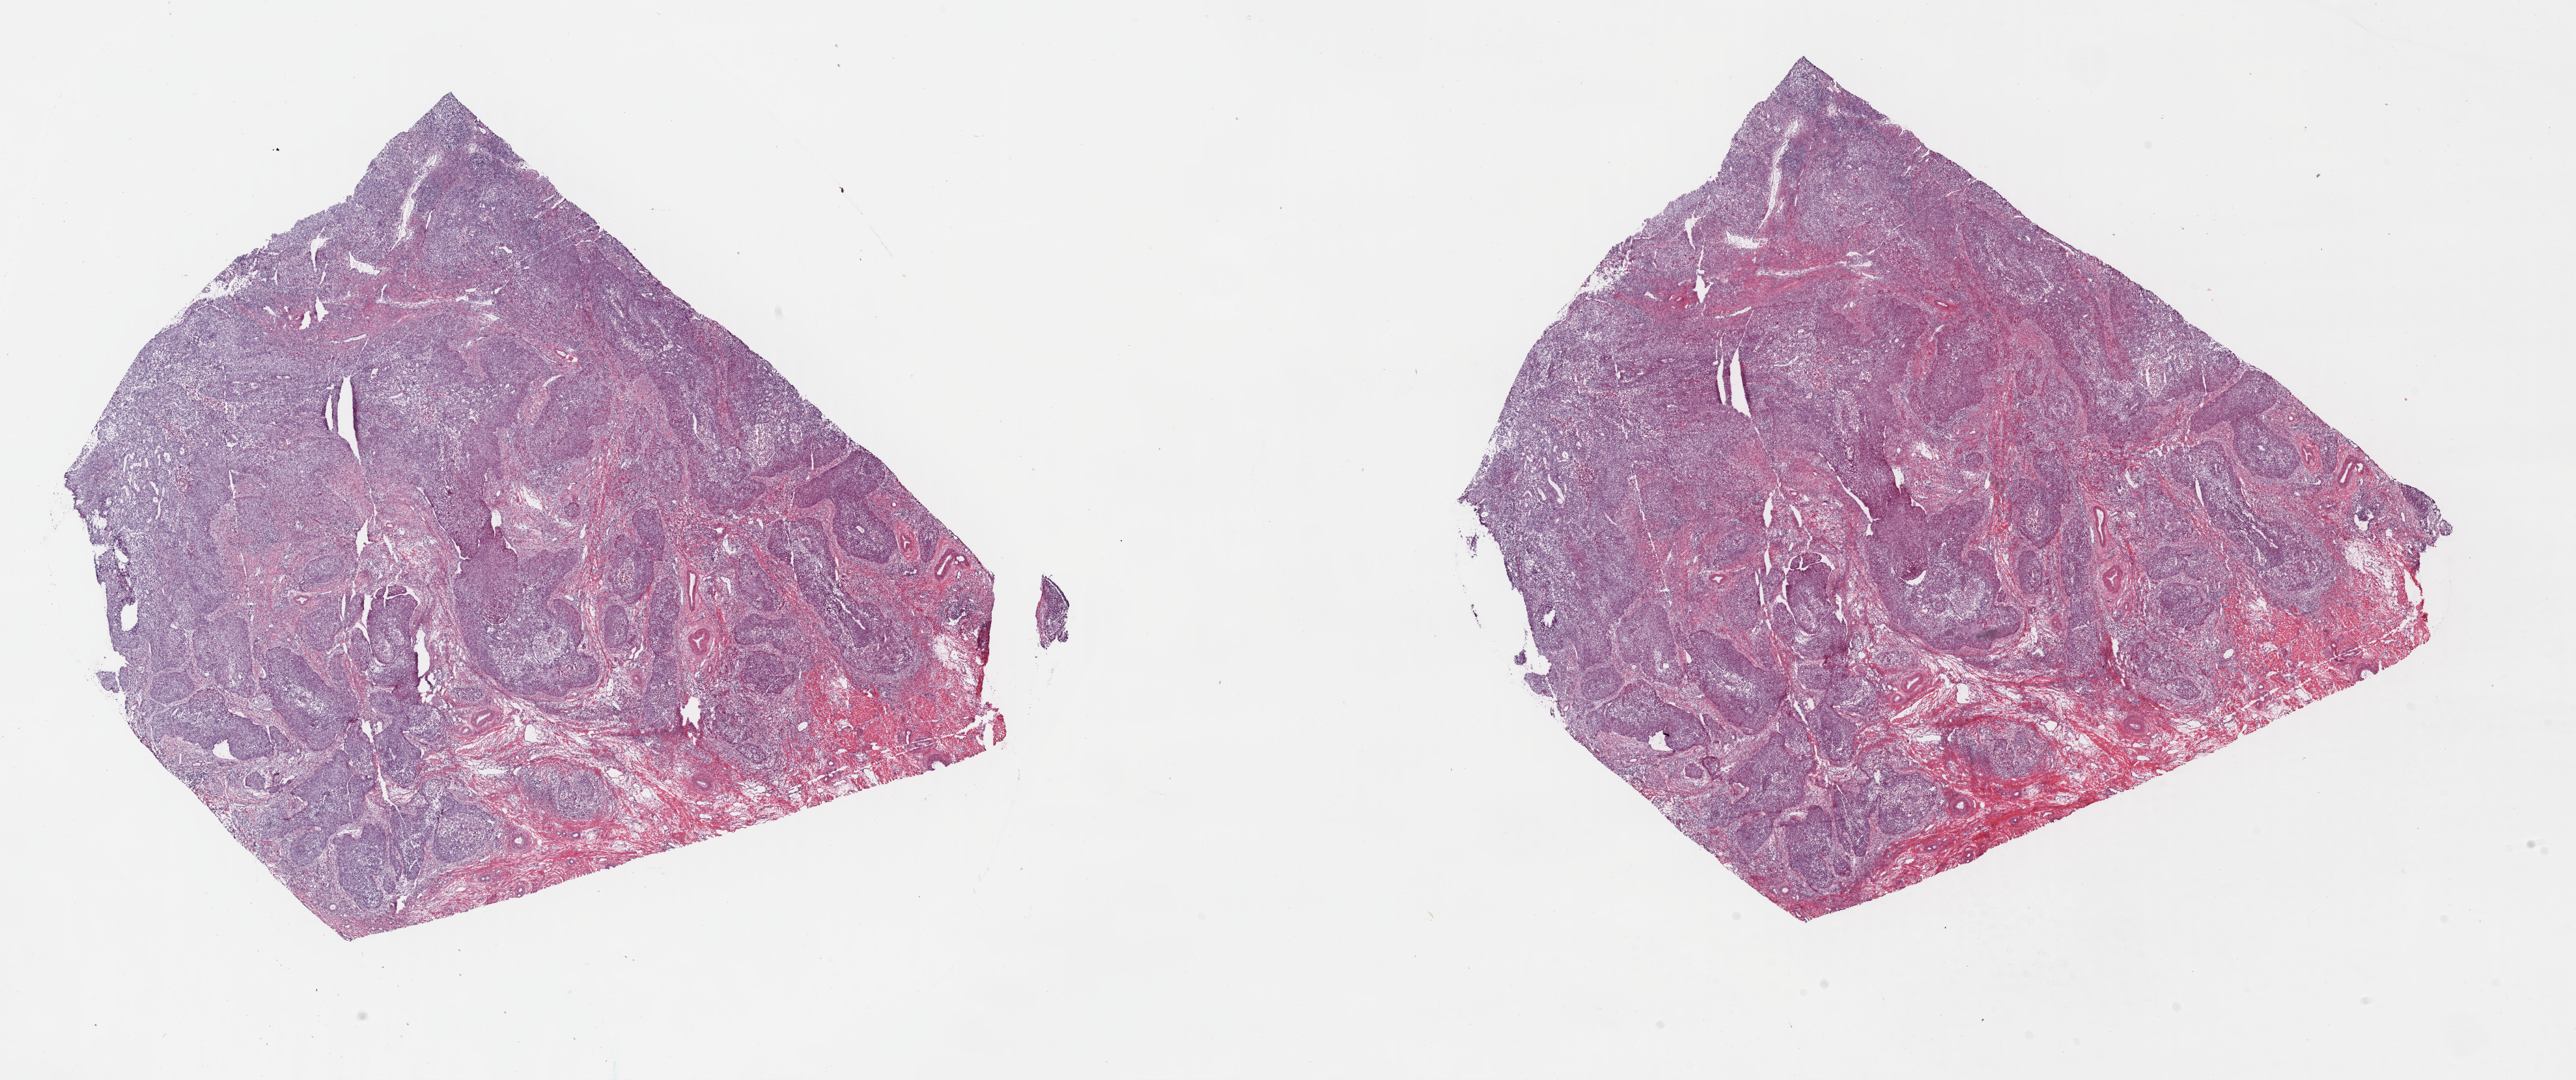
H&E whole-slide image, whole scanned area (about 31.1 x 13.0 mm, slide scanned at 40x) shown as a low-resolution overview, frozen section from the top of the tissue portion, cervix, primary tumour sample. Patient: female, age at initial diagnosis 40 years. Histologic grade: G2 (moderately differentiated). Slide review estimates, as recorded: tumour cells 60%, tumour nuclei 60%, normal cells 20%, stromal cells 20%, necrosis 0%. Infiltration values recorded for this section: lymphocyte infiltration 5%, monocyte infiltration 0%, neutrophil infiltration 0%.
FIGO stage: IB1. Histologic diagnosis: Squamous cell carcinoma, NOS.